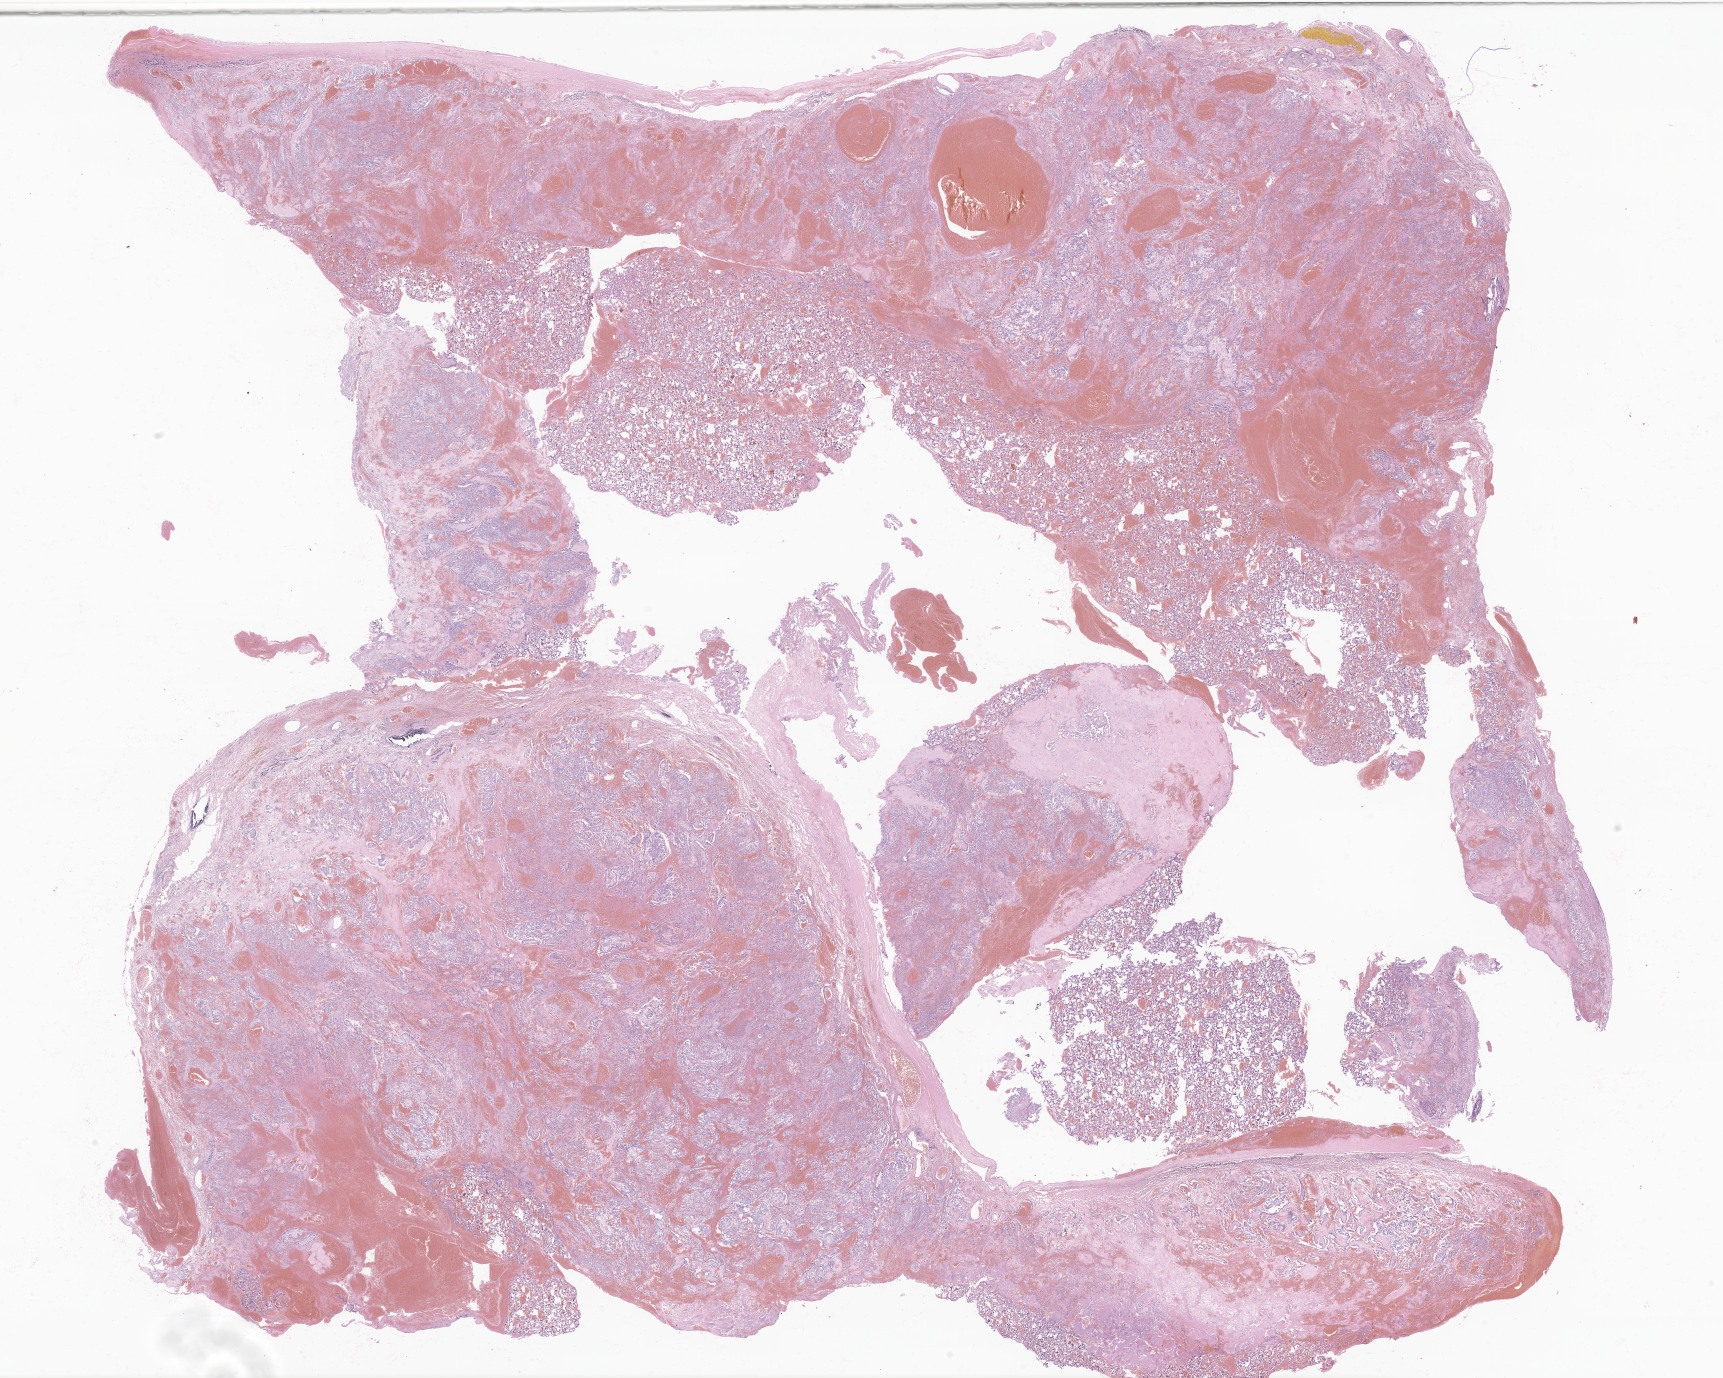
Digitized H&E-stained section of tumor tissue from the vertebral column — a low-resolution overview of the entire scanned area, about 29.1 x 23.2 mm. Formalin-fixed paraffin-embedded section. Female patient, age 188 months.
• recorded diagnosis: Neoplasm, uncertain whether benign or malignant